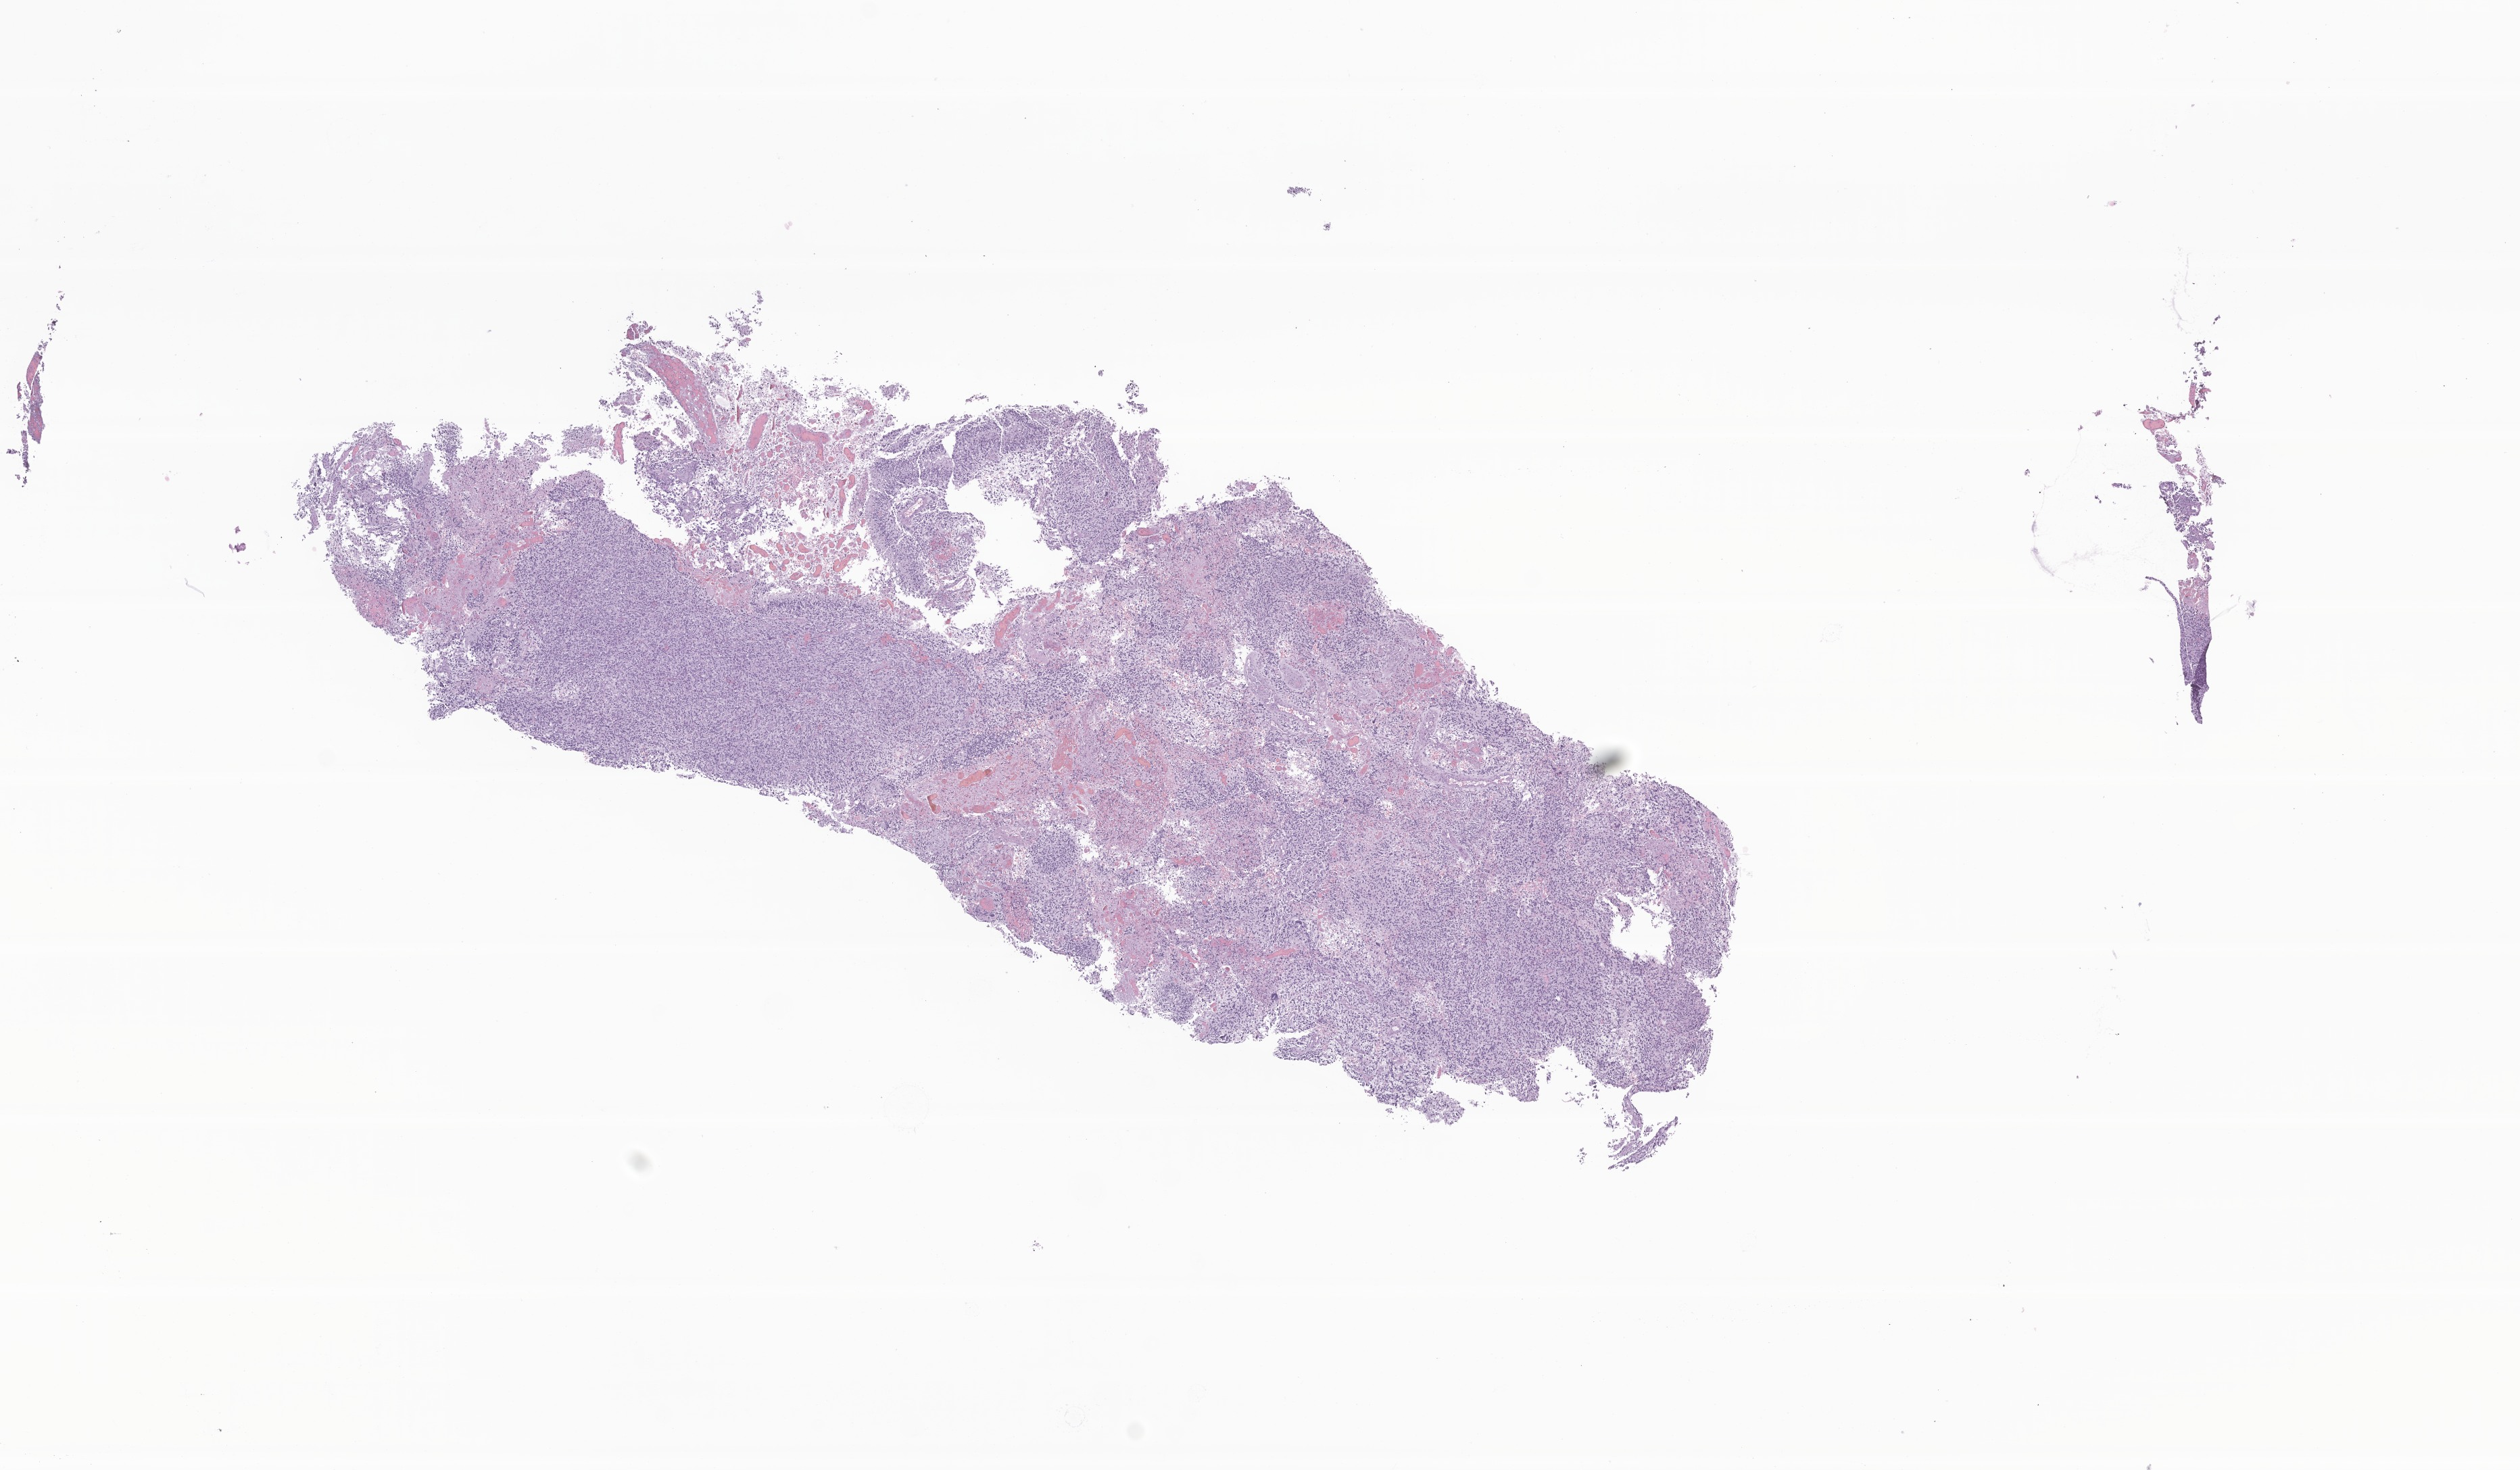
Digitized H&E-stained section of tumor tissue from the brain stem — shown as a low-resolution overview of the whole scanned area (about 15.7 x 9.2 mm); formalin-fixed, paraffin-embedded (FFPE) tissue. Patient: male, age 169 months (14 years 1 month).
Diagnosis: Glioma, malignant.